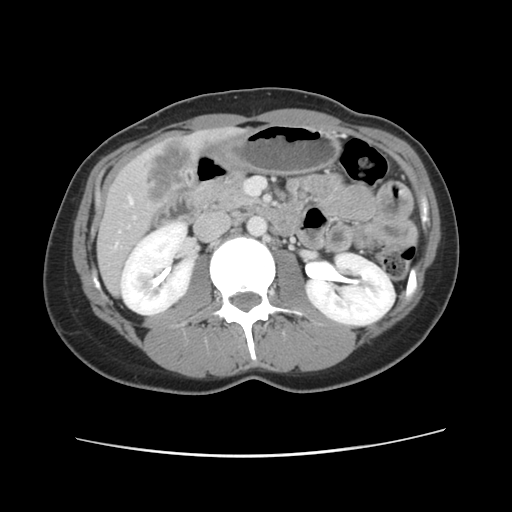
Contrast-enhanced abdominal CT, one axial slice; position 36 of 134 along the scan axis; 120 kVp; intravenous contrast given; soft-tissue window (W 400 / L 40 HU); 2.5 mm slice thickness; 512 × 512 image matrix, field of view 339 × 339 mm. Female patient, age 33 years. From the clinical record (not read from this slice): diagnosis: colorectal cancer liver metastases, imaged before liver resection; multiple liver metastases: yes; largest metastasis: 4.5 cm; disease in both lobes: yes.
Annotated regions visible in this slice (manually delineated by an expert):
- hepatic veins: bounding box (x1, y1, x2, y2) in pixels: (130, 198, 134, 204)
- liver: (98, 128, 237, 293)
- planned liver remnant (the part of the liver to remain after resection): (98, 242, 125, 293)
- liver metastasis: (148, 144, 198, 202)